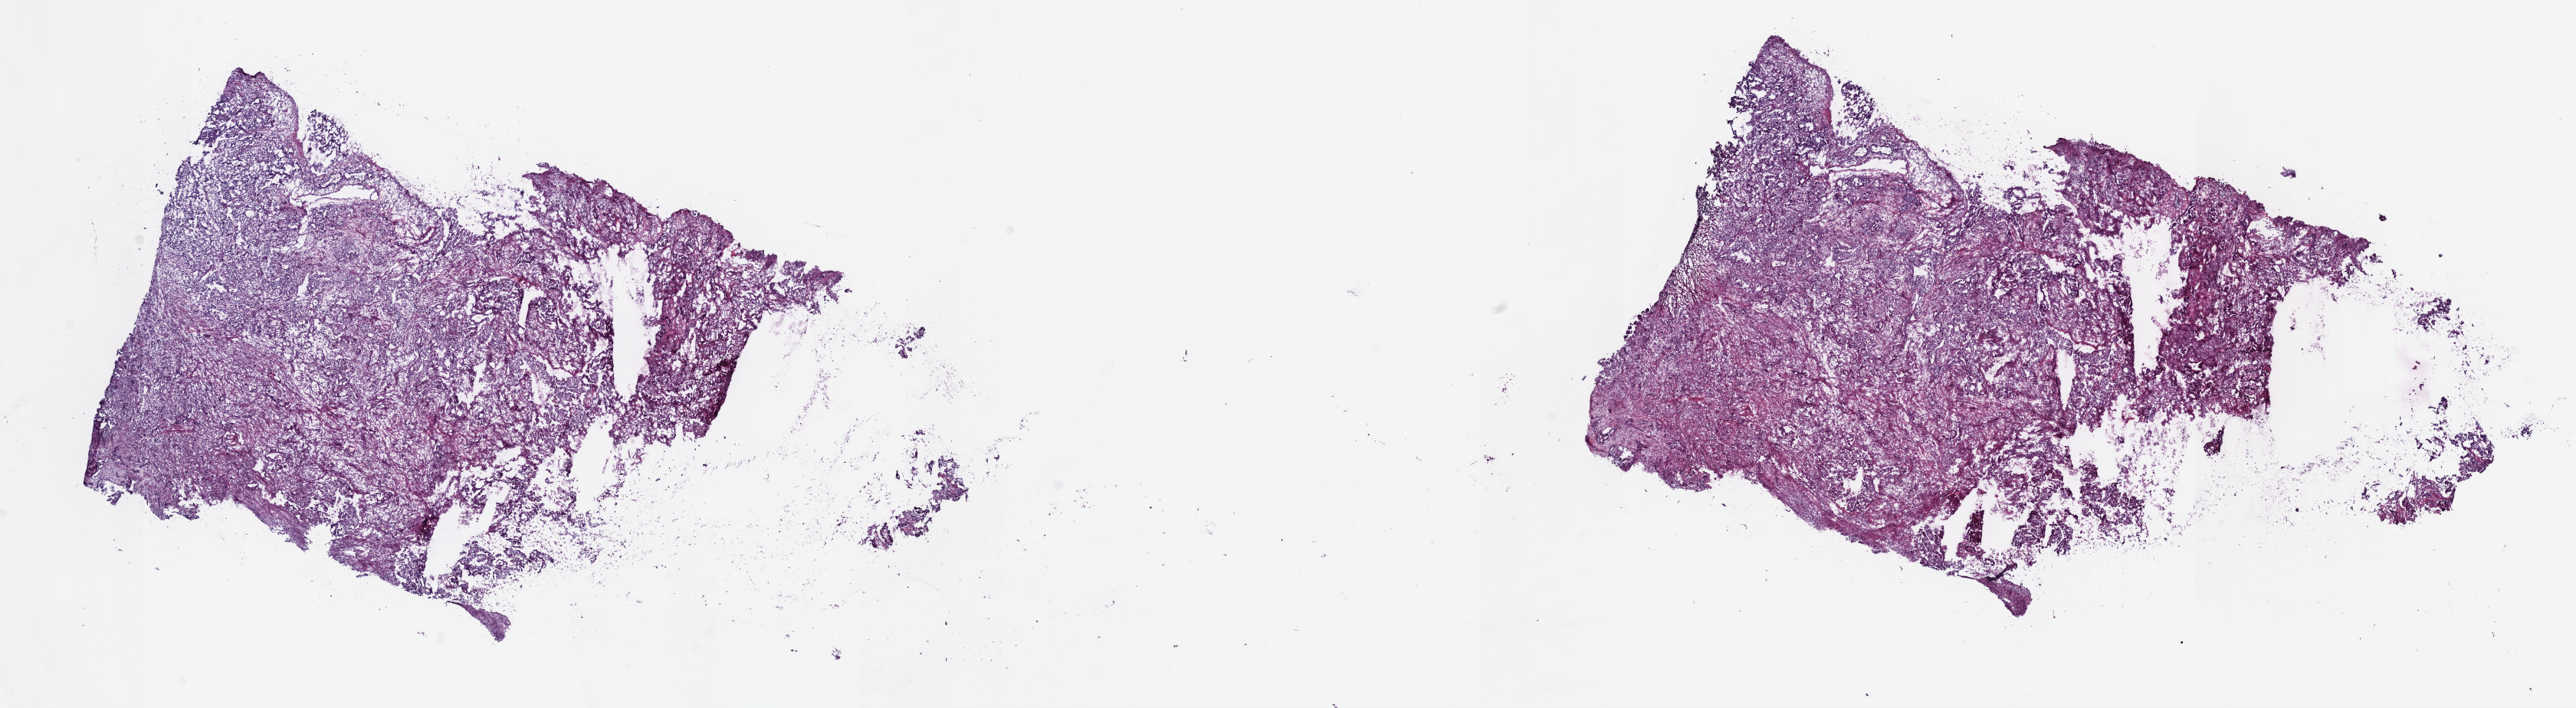
Whole-slide histology image, H&E, low-resolution overview of the scanned area, about 27.2 x 7.5 mm; frozen section from the top of the tissue portion; pancreas, primary tumour sample. Female, age 73 years at initial diagnosis. Histologic grade: G2 (moderately differentiated). Slide review estimates, as recorded: tumour cells 50%, tumour nuclei 60%, normal cells 0%, stromal cells 50%, necrosis 0%. Infiltration values recorded for this section: lymphocyte infiltration 0%, monocyte infiltration 0%, neutrophil infiltration 0%.
• histologic diagnosis: Adenocarcinoma, NOS (head of pancreas)
• lymph nodes positive (case pathology): 16 of 27 examined